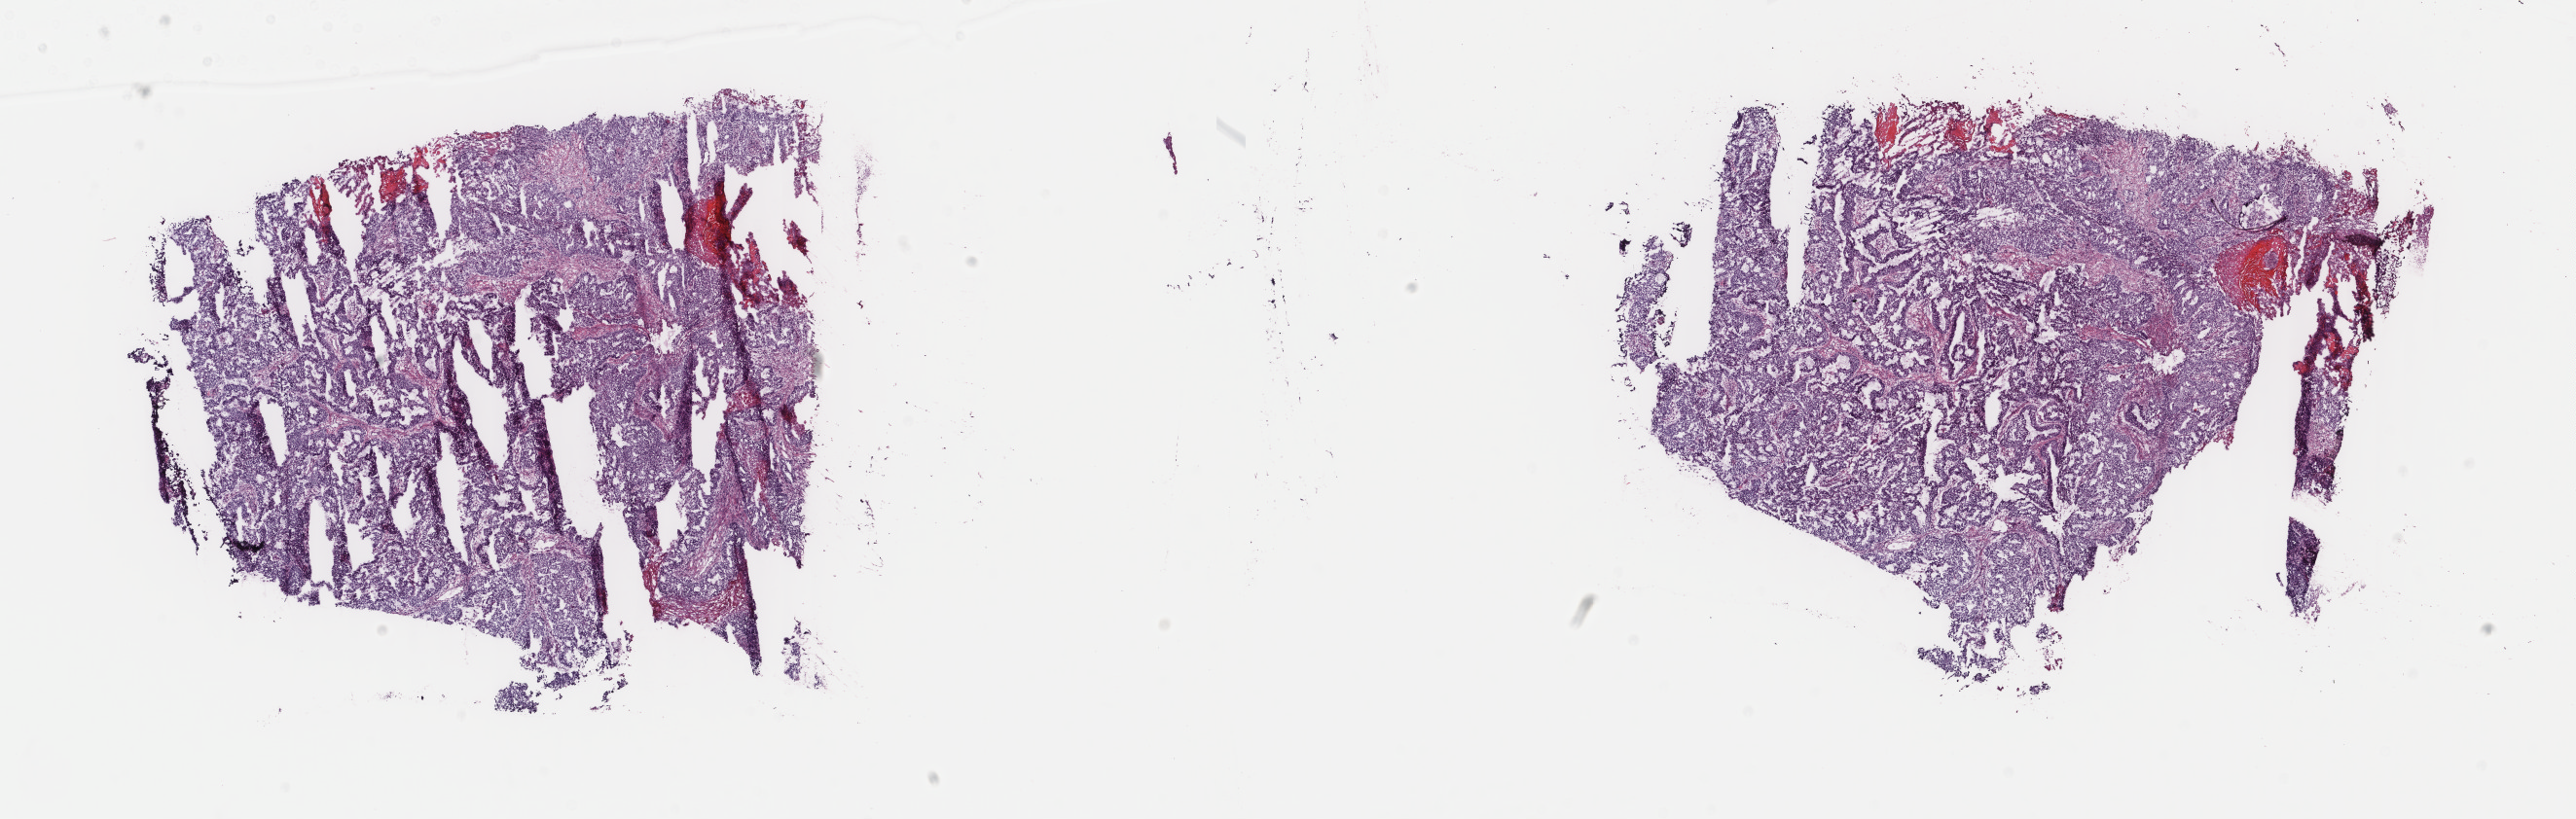
Hematoxylin and eosin (H&E) stained whole-slide image, low-resolution overview of the scanned area, about 21.0 x 6.7 mm. Frozen section from the top of the tissue portion. Primary tumour sample from the uterus. Female, age 44 years at initial diagnosis. Histologic grade: G3 (poorly differentiated). Composition of this section per pathologist review: tumour cells 80%, tumour nuclei 85%, normal cells 0%, stromal cells 15%, necrosis 5%. Infiltration values recorded for this section: lymphocyte infiltration 5%, monocyte infiltration 10%, neutrophil infiltration 8%.
• FIGO stage: IIIC
• histologic diagnosis: Endometrioid adenocarcinoma, NOS (endometrium)